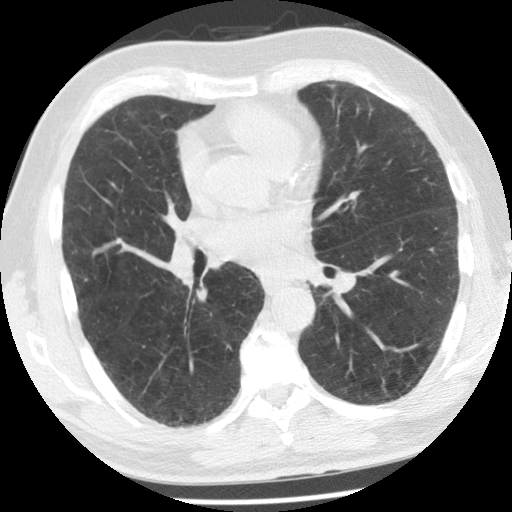
Low-dose screening chest CT, axial slice; baseline screening round; lung window (W 1500 / L -600 HU); 2.5 mm slice thickness; 512 × 512 image matrix, field of view 326 × 326 mm. Male participant, aged 66 years at enrolment. Former smoker at enrolment.
• Expert reader's lesion annotation, bounding box <304,69,353,112> (left, top, right, bottom; pixels).
• Reader record for this screening exam (exam-level; its link to the box is not recorded): non-calcified nodule or mass ≥4 mm, lingula, 5 × 4 mm, smooth margins, soft tissue attenuation.